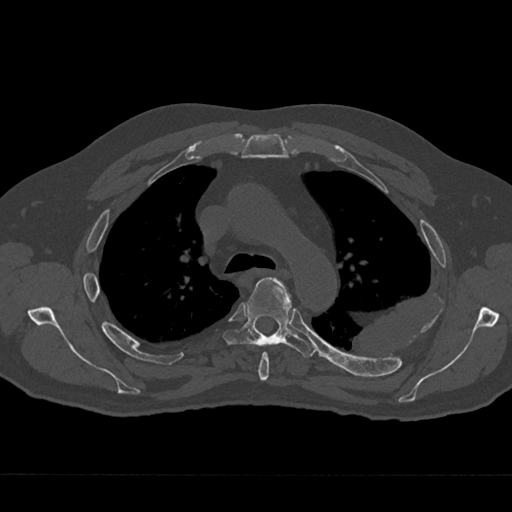
CT including the spine, one axial slice. Slice 487 of 797 in the series (ordered by position). 120 kVp. Bone window (W 1800 / L 400 HU). 0.5 mm slice thickness. 512 × 512 image matrix, field of view 377 × 377 mm. Patient: male, 75 years. Case-level facts recorded for this patient, not image findings: primary cancer: renal; vertebrae with lytic lesions (as recorded): T4.
Structures marked on this image (semi-automatically segmented with operator editing):
- T4 vertebra: bounding box [x1, y1, x2, y2] px = [258, 352, 269, 381]
- T5 vertebra: [222, 277, 317, 358]